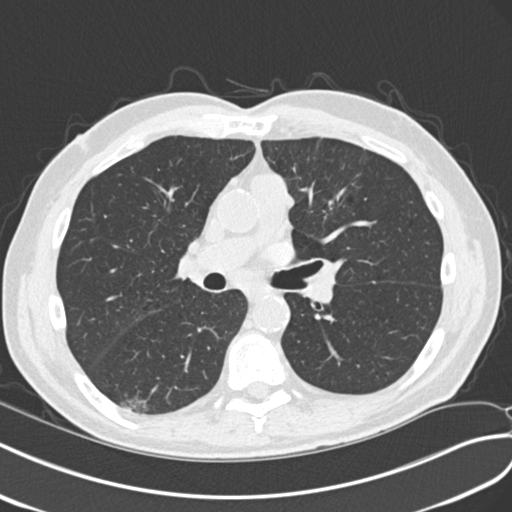
Axial slice from a low-dose chest CT screening exam, second screening round (one year after baseline), lung window (W 1500 / L -600 HU), 2 mm slice thickness, standard (soft-tissue) reconstruction kernel (B30f), 120 kVp, slice 102 of 240 in the series, 512 × 512 image matrix, field of view 354 × 354 mm. Male, age 68 years at enrolment. Current smoker at enrolment.
Expert-annotated lung lesion, box from (x=113, y=386) to (x=162, y=422) px. The screening reader recorded 4 non-calcified nodules or masses ≥4 mm on this exam (right upper lobe, left upper lobe, right upper lobe, right lower lobe); which of them this box marks is not recorded. Lung cancer was diagnosed 653 days after this screen: non-small cell carcinoma, right lower lobe, poorly differentiated (G3), stage IA (AJCC 6th edition), 23 mm at pathology.